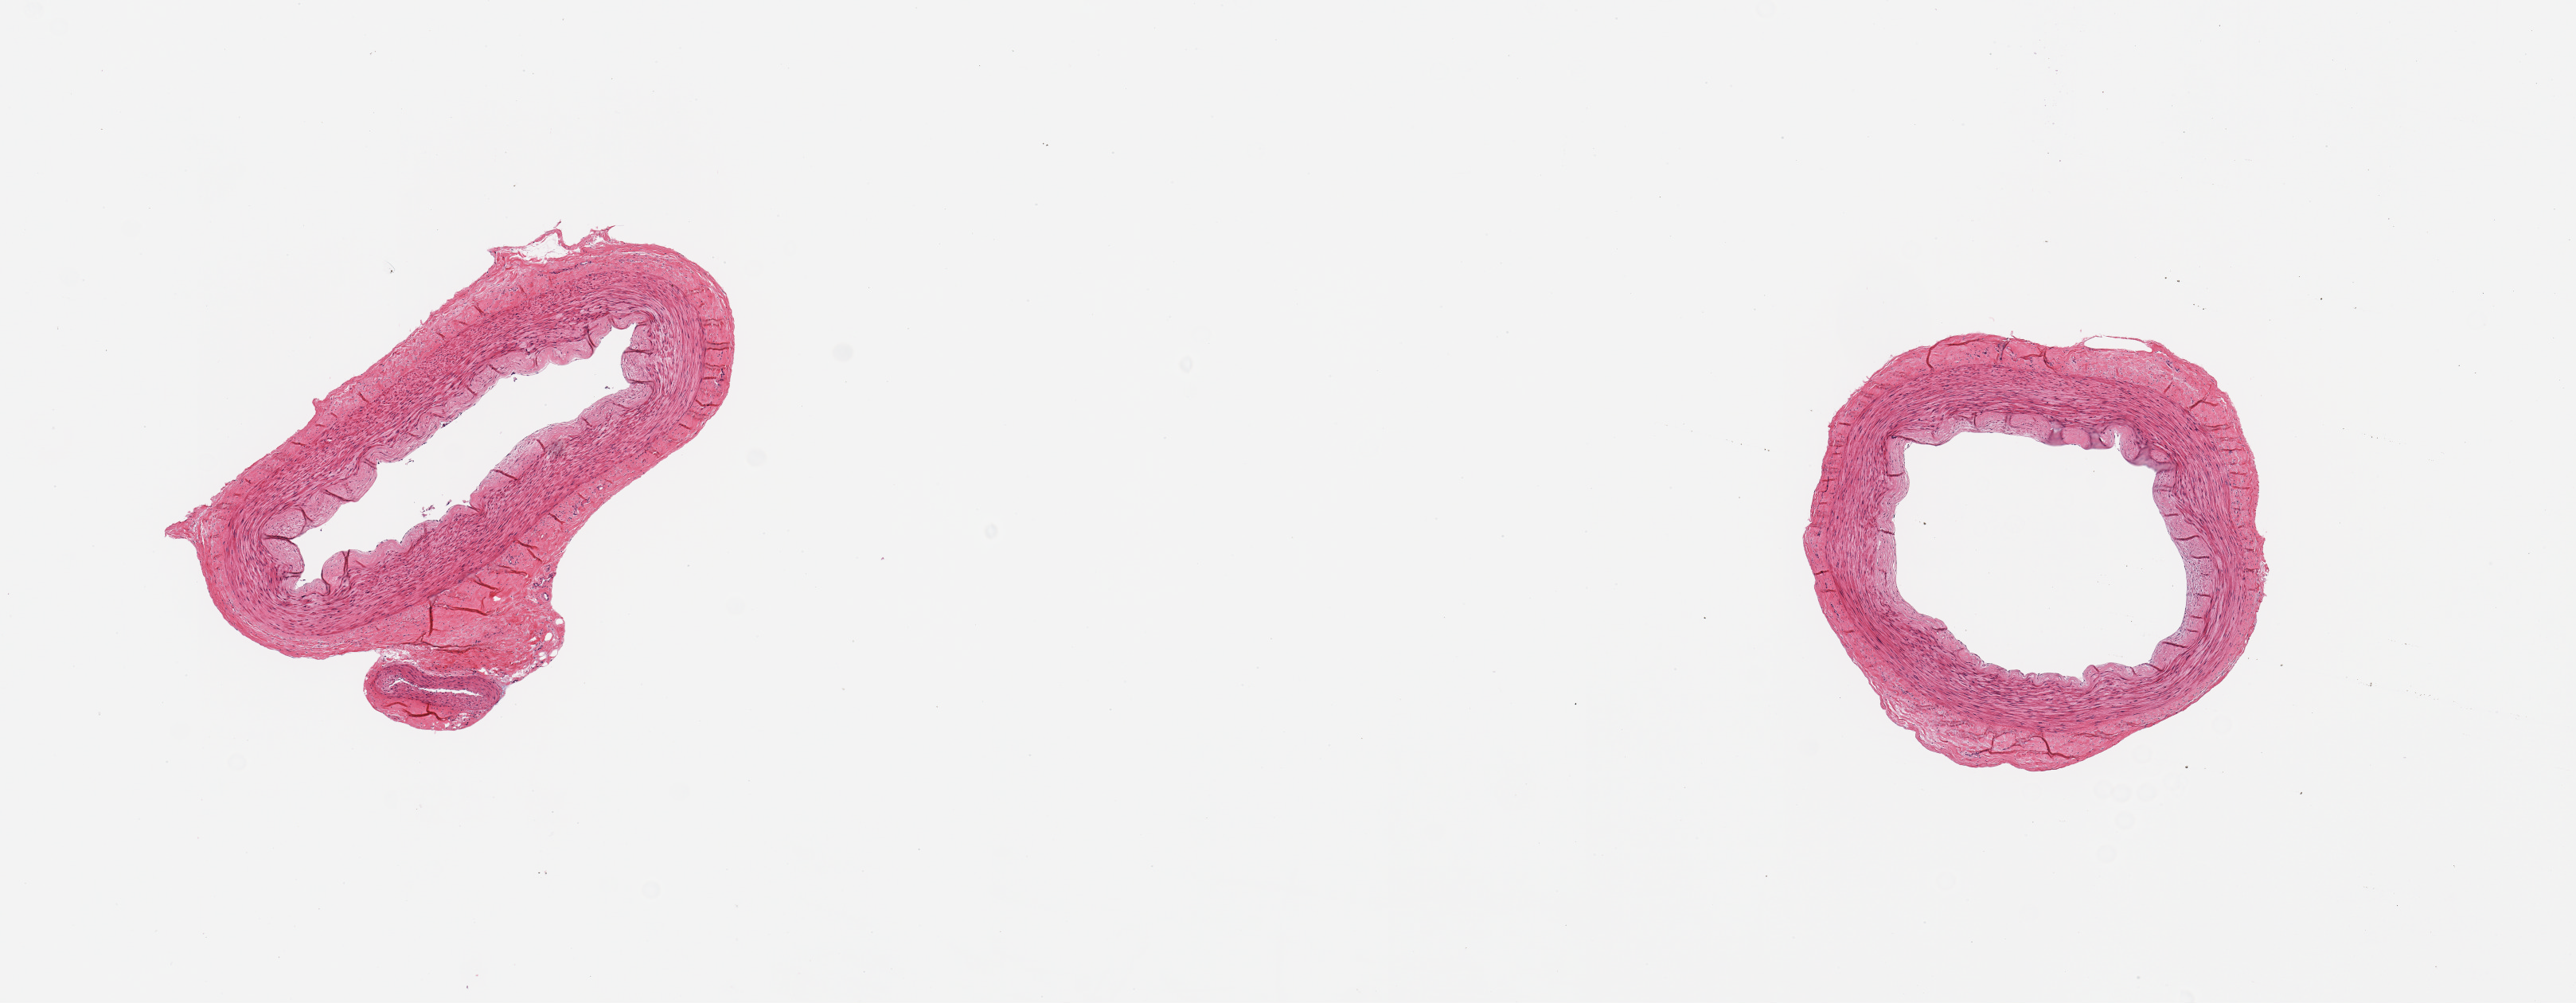
H&E whole-slide image, brightfield — a low-resolution overview of the entire scanned area, about 12.8 x 5.0 mm; PAXgene-fixed, paraffin-embedded tissue; target tissue: tibial artery; tissue donor sample. Donor: male.
Reviewer comment on this tissue sample: 2 pieces, no adherent fat.